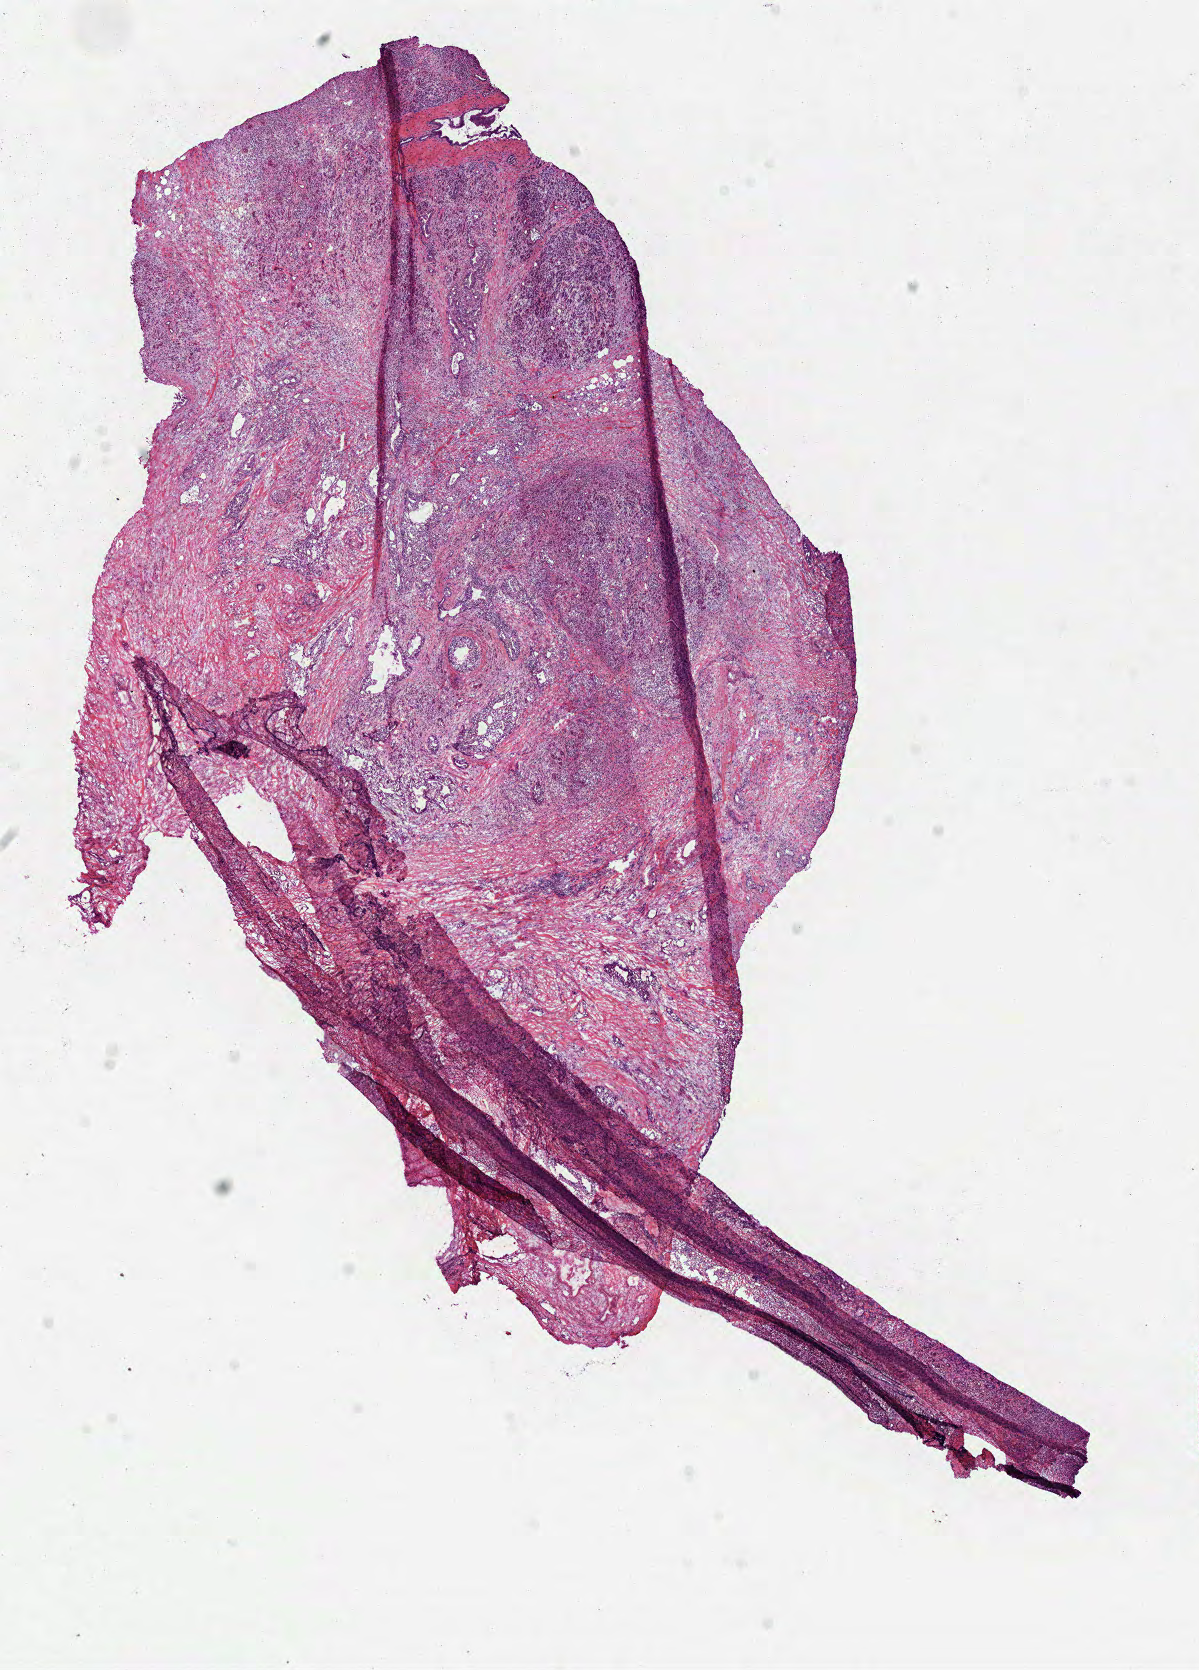
Whole-slide histology image, Hematoxylin and eosin (H&E) stained — a low-resolution overview of the entire scanned area, about 9.7 x 13.5 mm; frozen section from the bottom of the tissue portion; primary tumour sample from the pancreas. Male, age 59 years at initial diagnosis. Histologic grade: G2 (moderately differentiated). Pathologist review of this section (percent, as recorded): tumour cells 55%, tumour nuclei 60%, normal cells 30%, stromal cells 15%, necrosis 0%. Infiltration values recorded for this section: lymphocyte infiltration 30%, monocyte infiltration 0%, neutrophil infiltration 0%.
AJCC pathologic stage: IIB. Lymph nodes positive (case pathology): 3 of 24 examined. Histologic diagnosis: Infiltrating duct carcinoma, NOS (head of pancreas).